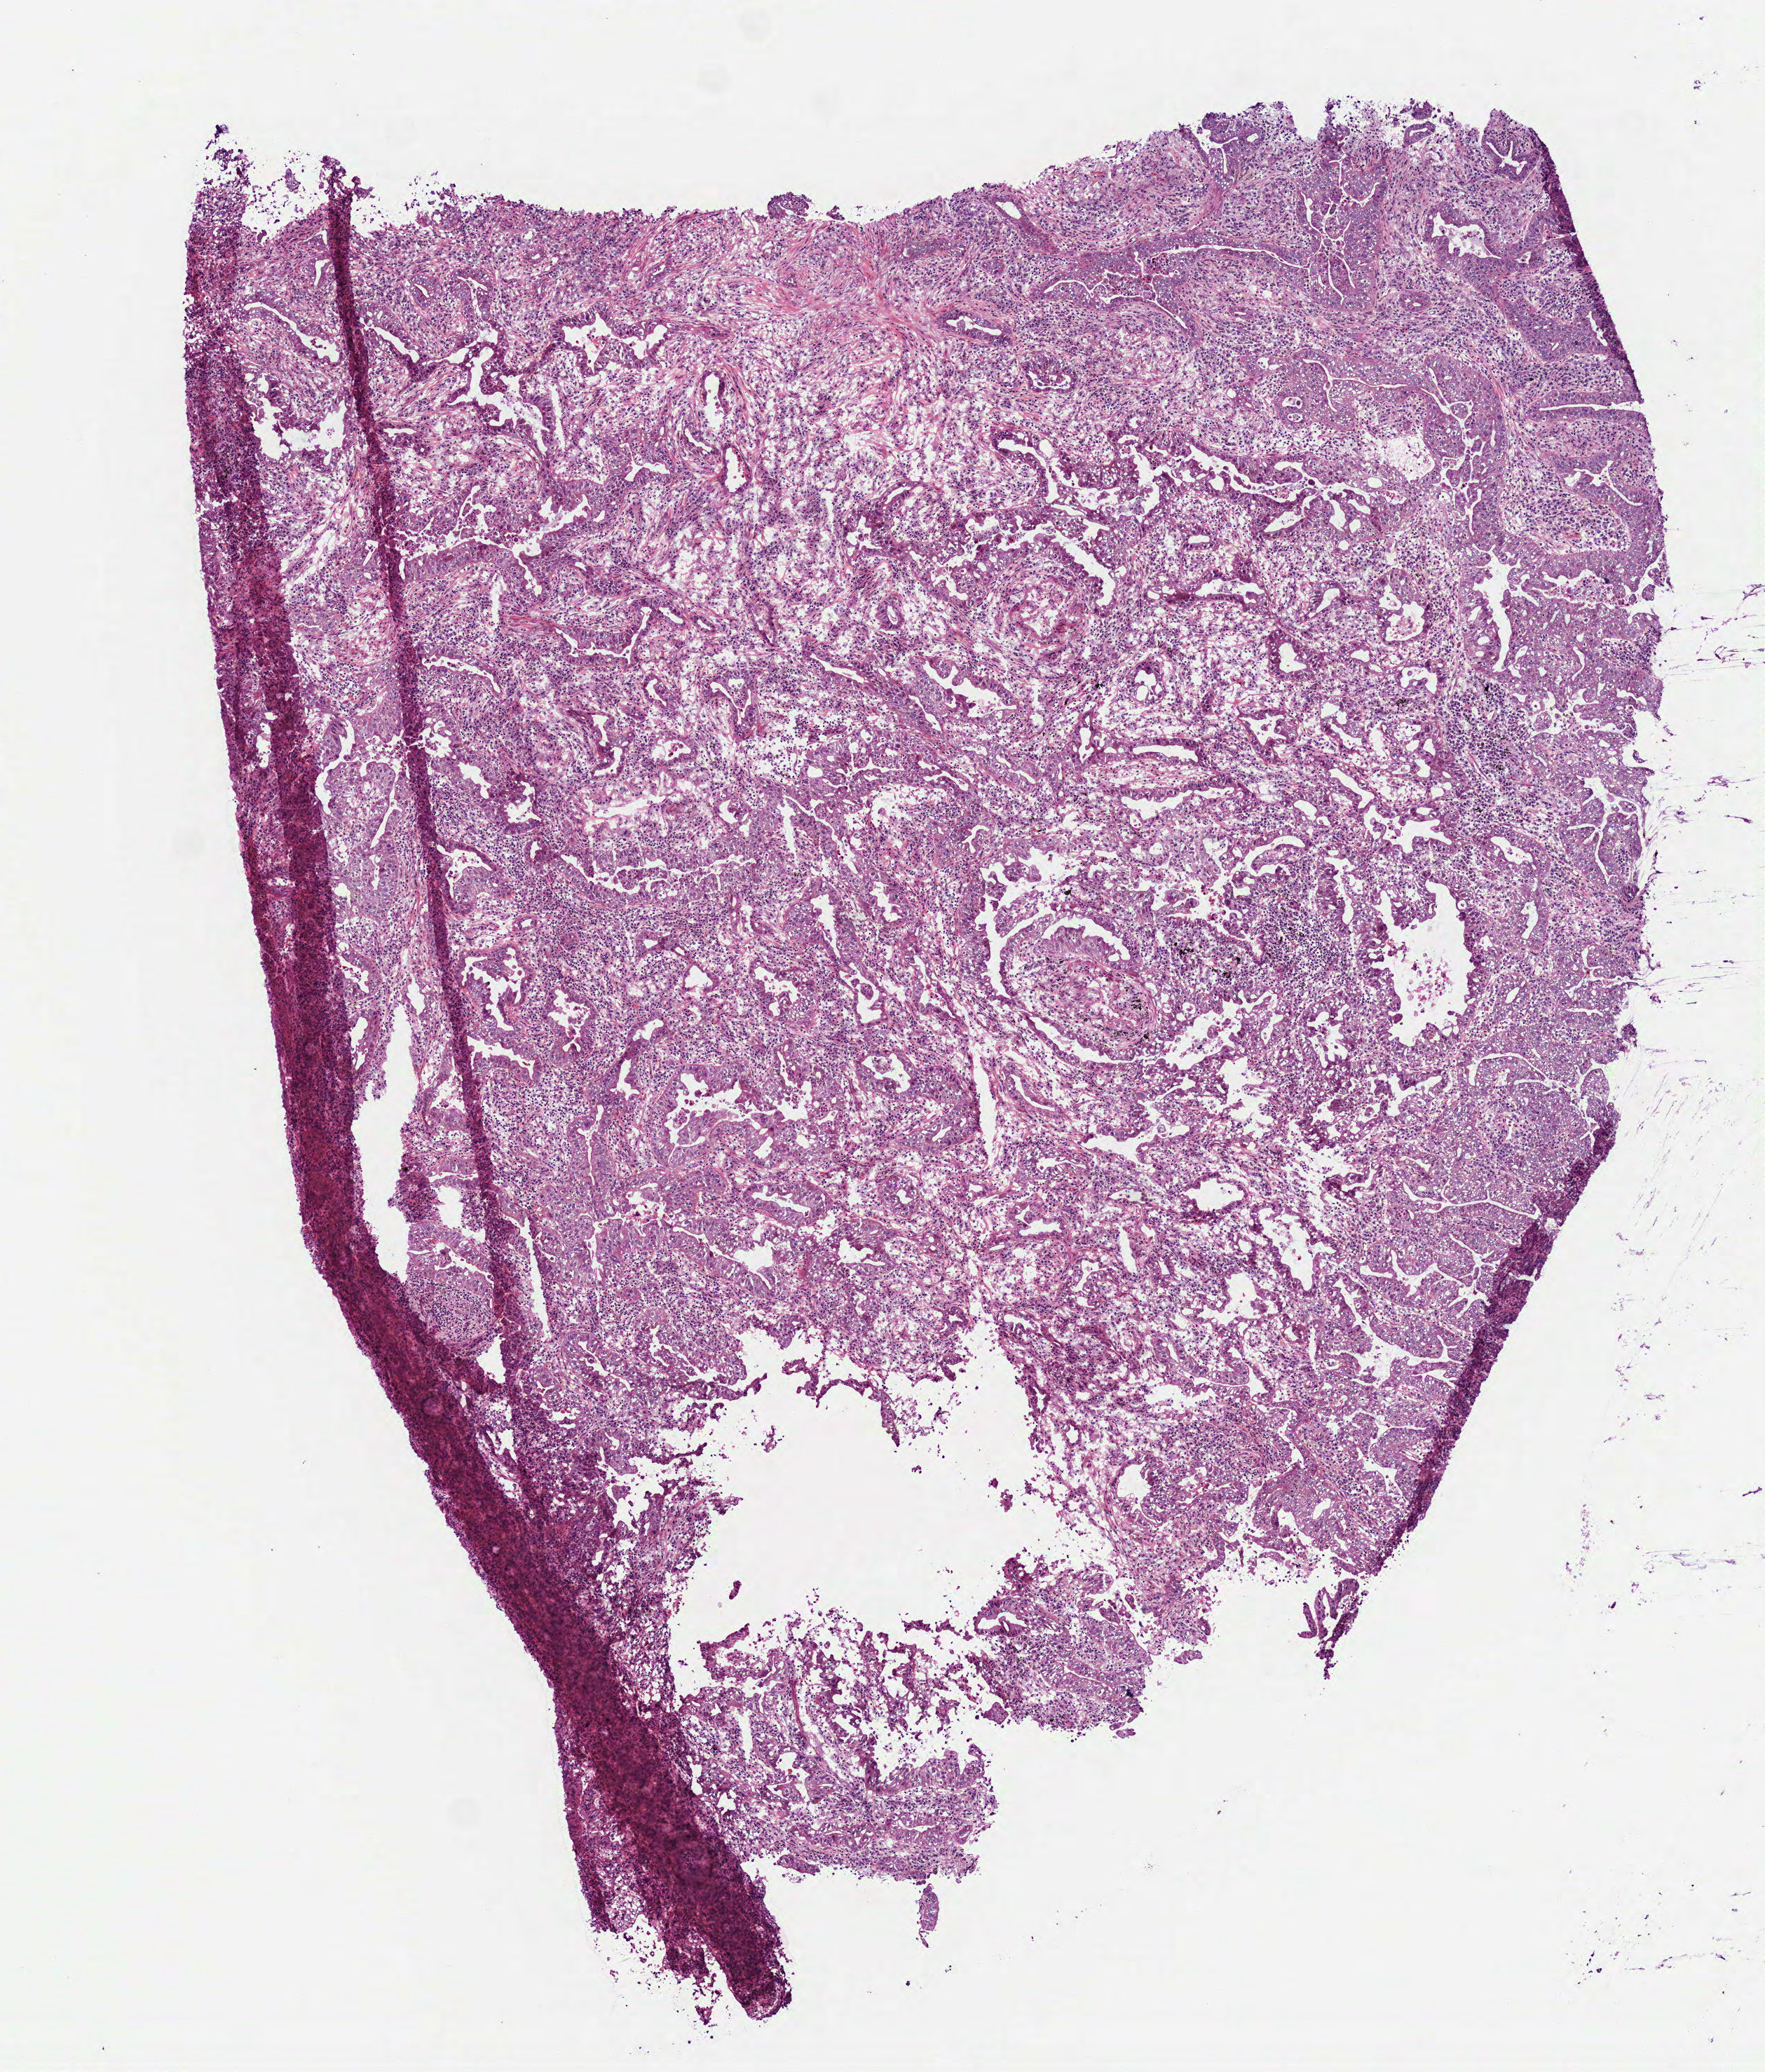
Digitized Hematoxylin and eosin (H&E) stained tissue section (whole slide) — low-resolution overview of the scanned area, about 5.1 x 6.0 mm (slide scanned at 40x). Frozen section from the top of the tissue portion. Sample: primary tumour, lung. Male, age 84 years at initial diagnosis. Pathologist review of this section (percent, as recorded): tumour cells 90%, tumour nuclei 60%, normal cells 0%, stromal cells 10%, necrosis 0%. Infiltration values recorded for this section: lymphocyte infiltration 30%.
Diagnosis: Acinar cell carcinoma (lower lobe, lung). AJCC pathologic stage: IB.